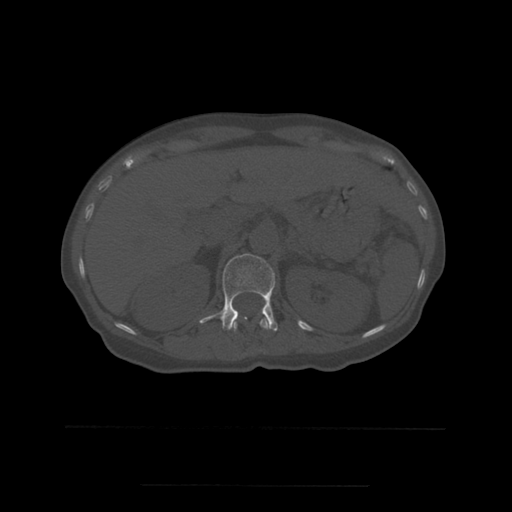
CT including the spine, one axial slice. Slice 243 of 544 in the series (ordered by position). Bone window (W 1800 / L 400 HU). 512 × 512 image matrix, field of view 350 × 350 mm. Patient age 58 years. From the clinical record (not read from this slice): primary cancer: lung.
Structures marked on this image (semi-automatic segmentation, software-assisted and operator-edited):
- L1 vertebra: bounding box [x1, y1, x2, y2] px = [199, 254, 278, 332]
- T12 vertebra: [233, 317, 270, 331]